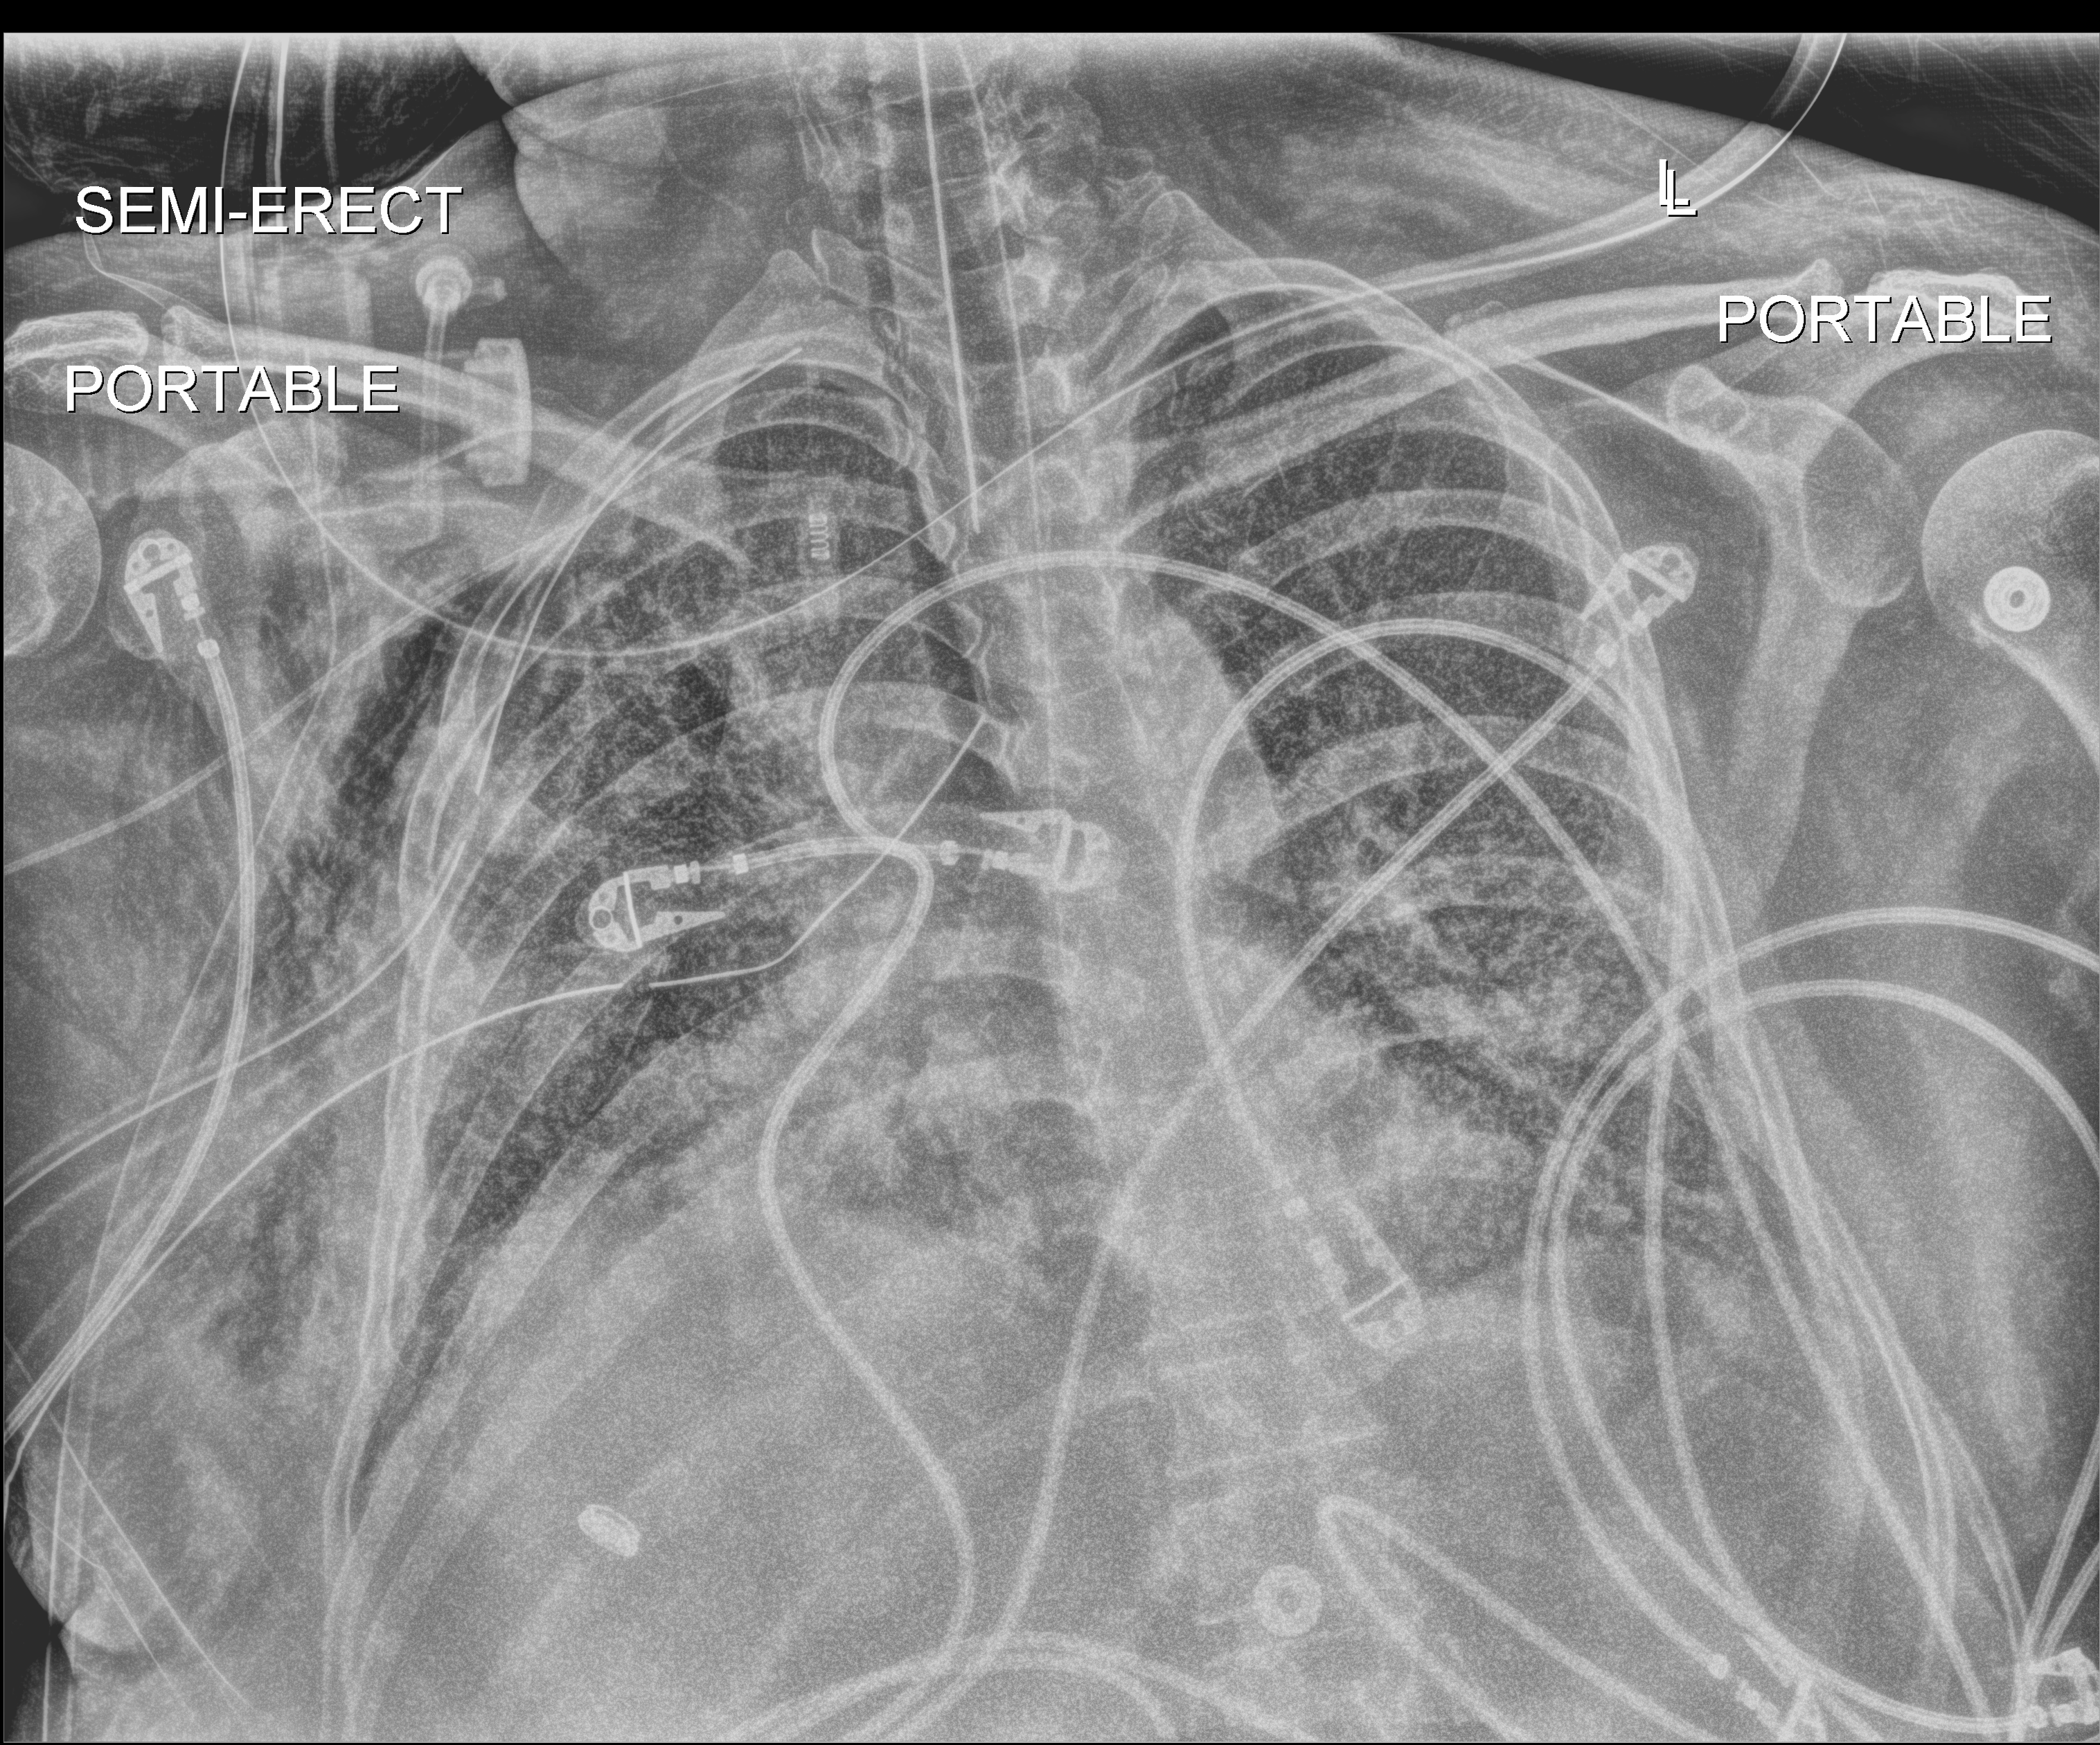
Portable chest radiograph; anteroposterior (AP) projection. Adult patient hospitalised with COVID-19, age 18–59 years.
Hospital-stay facts (about this admission, not read from this image; timing relative to this image not recorded):
- mechanically ventilated during this hospital stay: yes
- admitted to intensive care during this hospital stay: yes
- length of hospital stay: 48 days